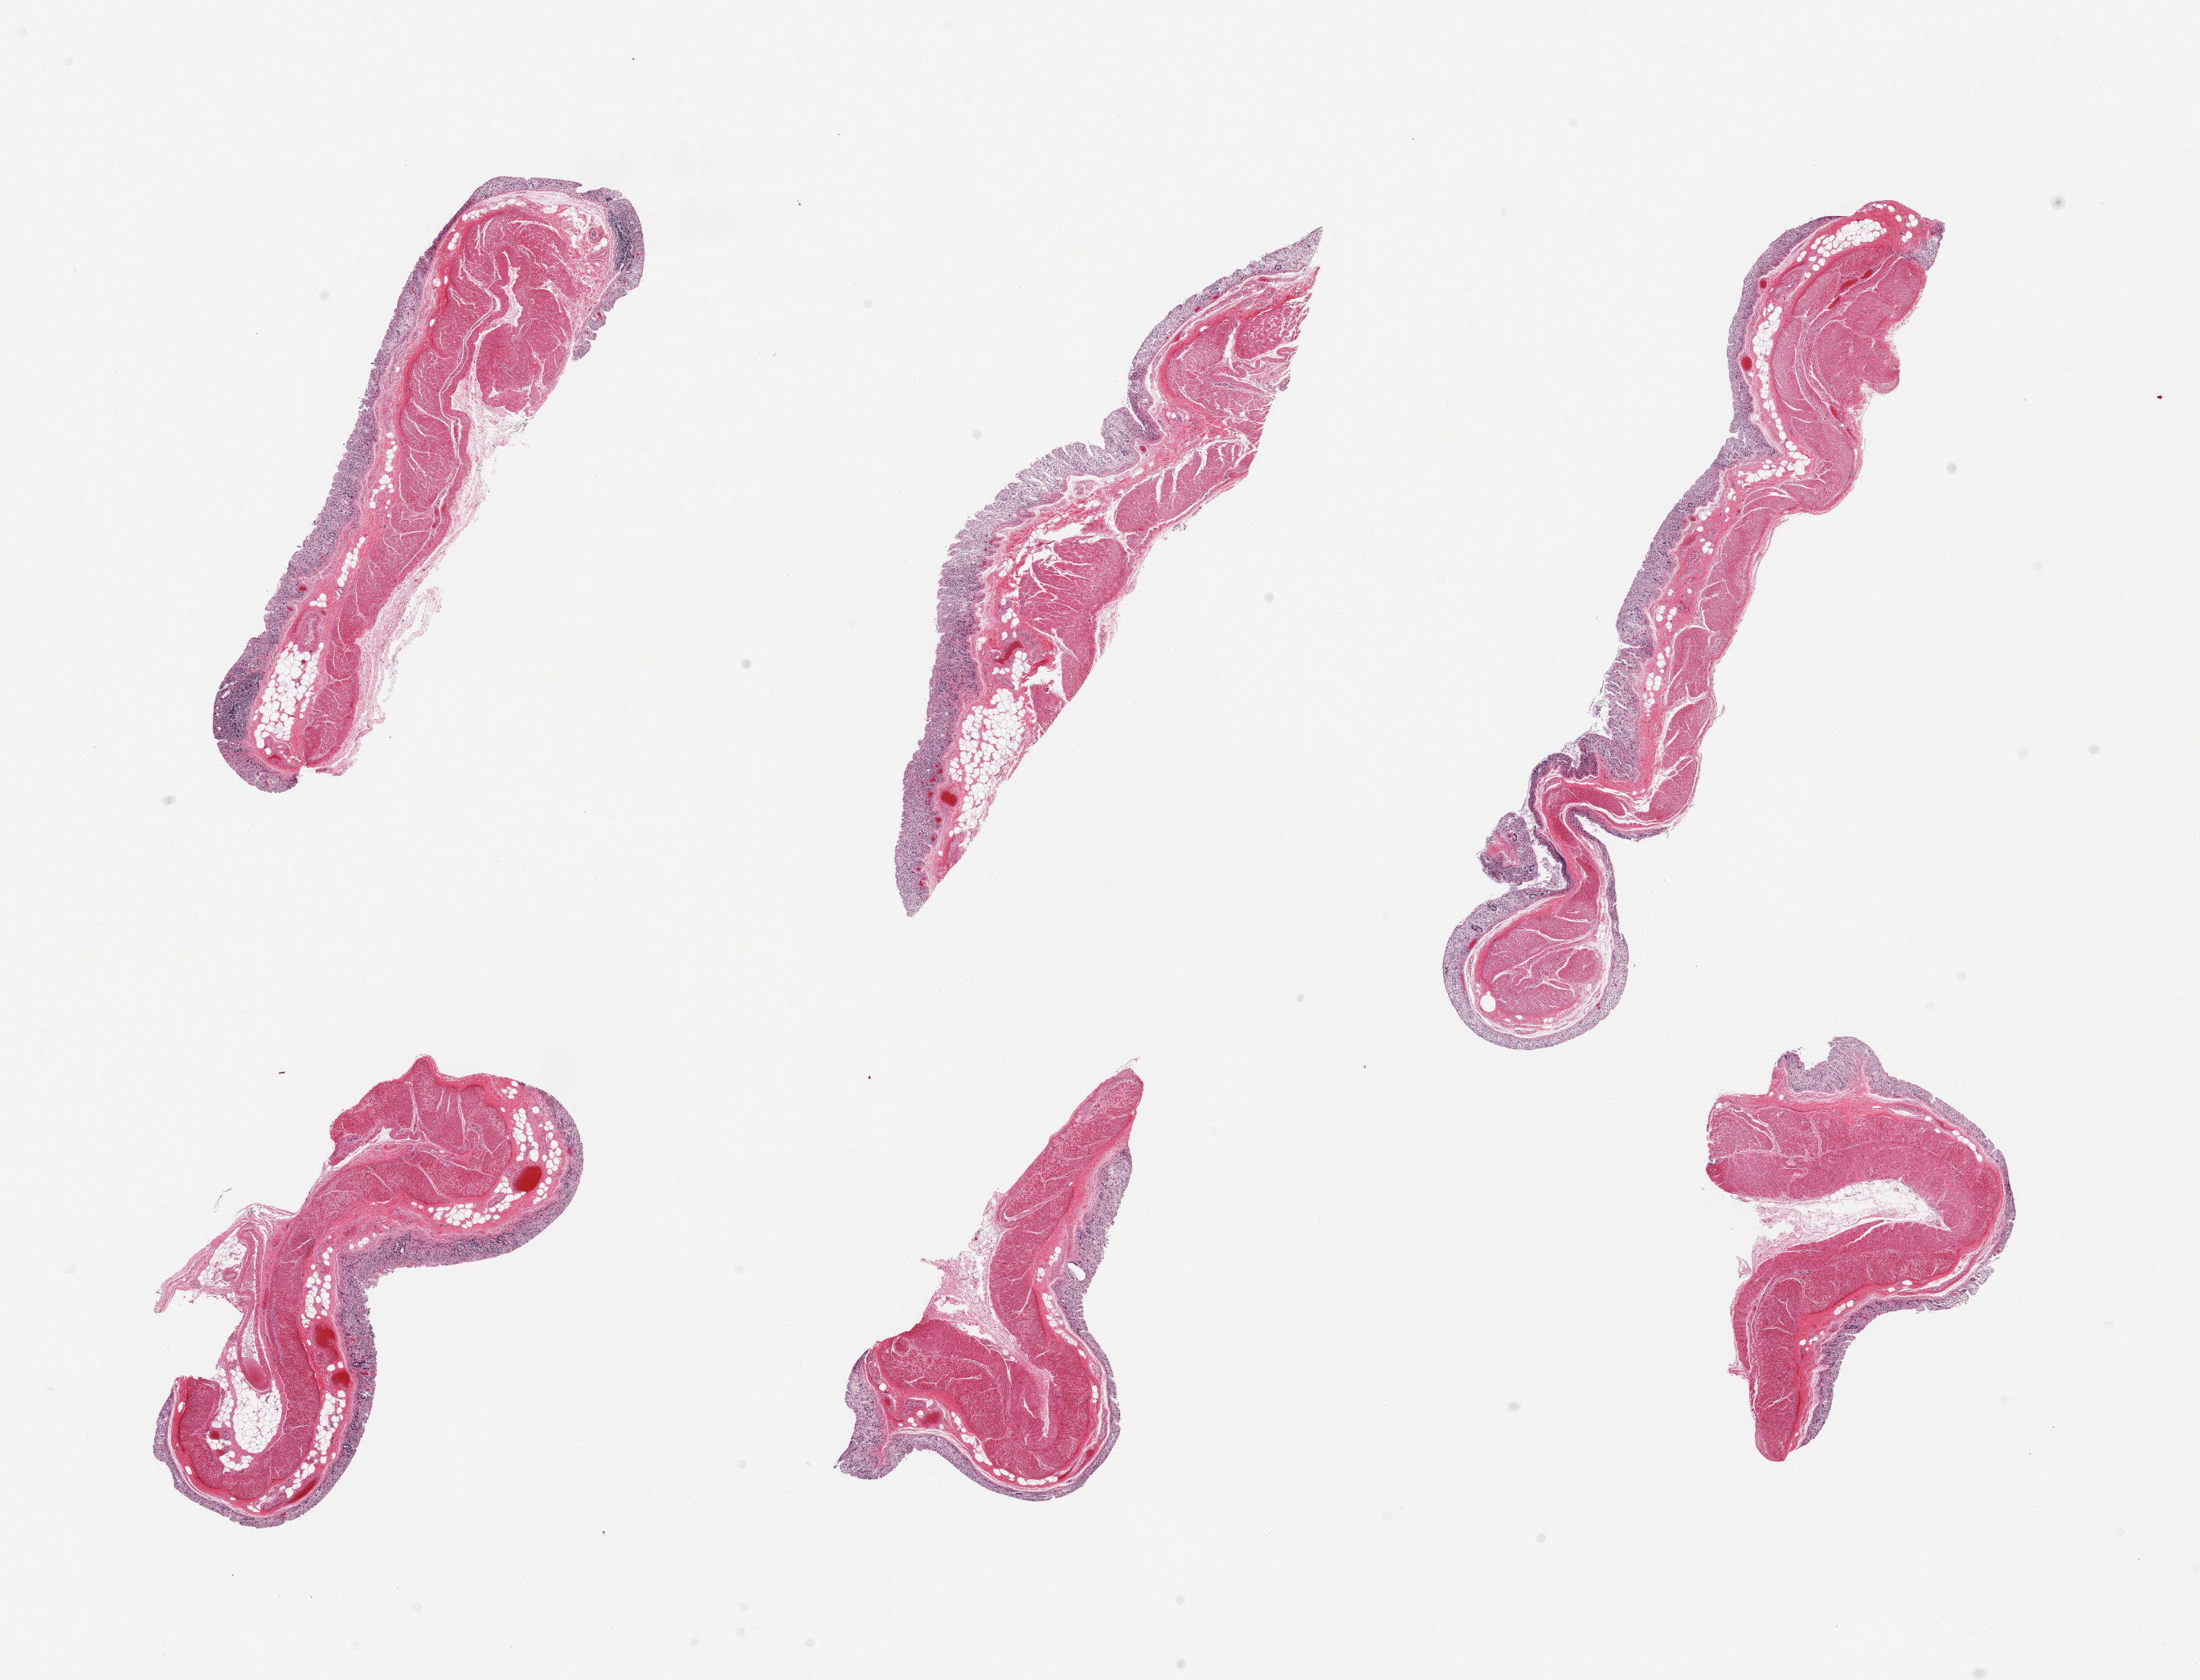
Digitized haematoxylin and eosin-stained section, brightfield — low-resolution overview of the scanned area, about 21.7 x 16.5 mm (acquisition: 20x scan); PAXgene-fixed paraffin-embedded (PFPE) section; sampled site (target tissue): transverse colon; donor tissue sample.
Pathologist's review note for this sample: 6 pieces, mucosa up to ~0.3 mm, severely autolyzed.